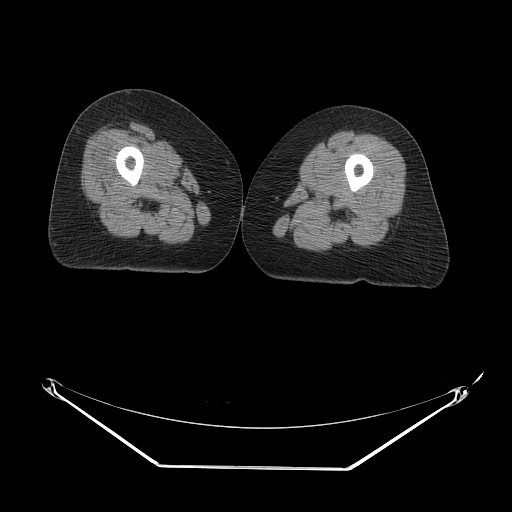
CT of an extremity soft-tissue mass (from a PET/CT study), one axial slice. Slice 9 of 267 in the series (ordered by position). Soft-tissue window (W 400 / L 40 HU). 3.75 mm slice thickness. 512 × 512 image matrix, field of view 500 × 500 mm. Female patient. Case-level facts recorded for this patient, not image findings: histological type: malignant solitary fibrous tumor; grade: intermediate; site of the primary tumour: right thigh.
Structures marked on this image (expert contour drawn on MRI and transferred to this co-registered scan by the dataset authors):
- gross tumour volume including surrounding oedema: bounding box <165,145,168,147> (left, top, right, bottom; pixels)